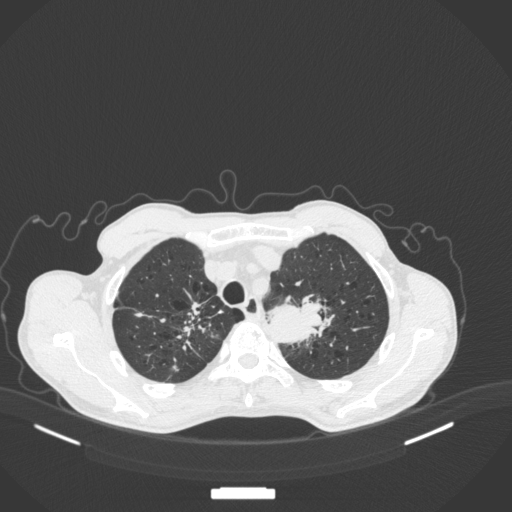
Chest CT, one axial slice; slice 354 of 394 in the series (ordered by position); reconstruction kernel B31f; lung window (W 1500 / L -600 HU); 1 mm slice thickness; 512 × 512 image matrix. Male patient, age 65 years. Case-level facts recorded for this patient, not image findings: clinical TNM (as recorded): T2b N0 M0; histopathological grade: G2.
Annotated regions visible in this slice (rectangle marked by the reading radiologist):
- lung tumour (recorded histology: adenocarcinoma): bounding box <264,284,330,346> (left, top, right, bottom; pixels)